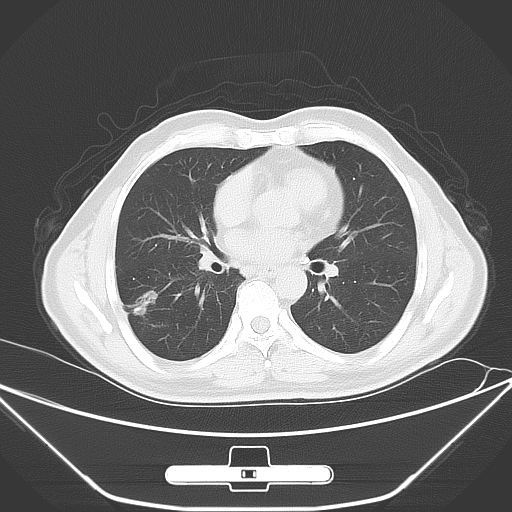
Chest CT, one axial slice; position 29 of 62 along the scan axis; 120 kVp; lung window (W 1500 / L -600 HU); 512 × 512 image matrix. Patient: male, 71 years. From the clinical record (not read from this slice): clinical TNM (as recorded): T1c N0 M0; histopathological grade: G2.
Outlined on this slice (rectangle marked by the reading radiologist):
- lung tumour (recorded histology: adenocarcinoma): bounding box <125,286,163,323> (left, top, right, bottom; pixels)